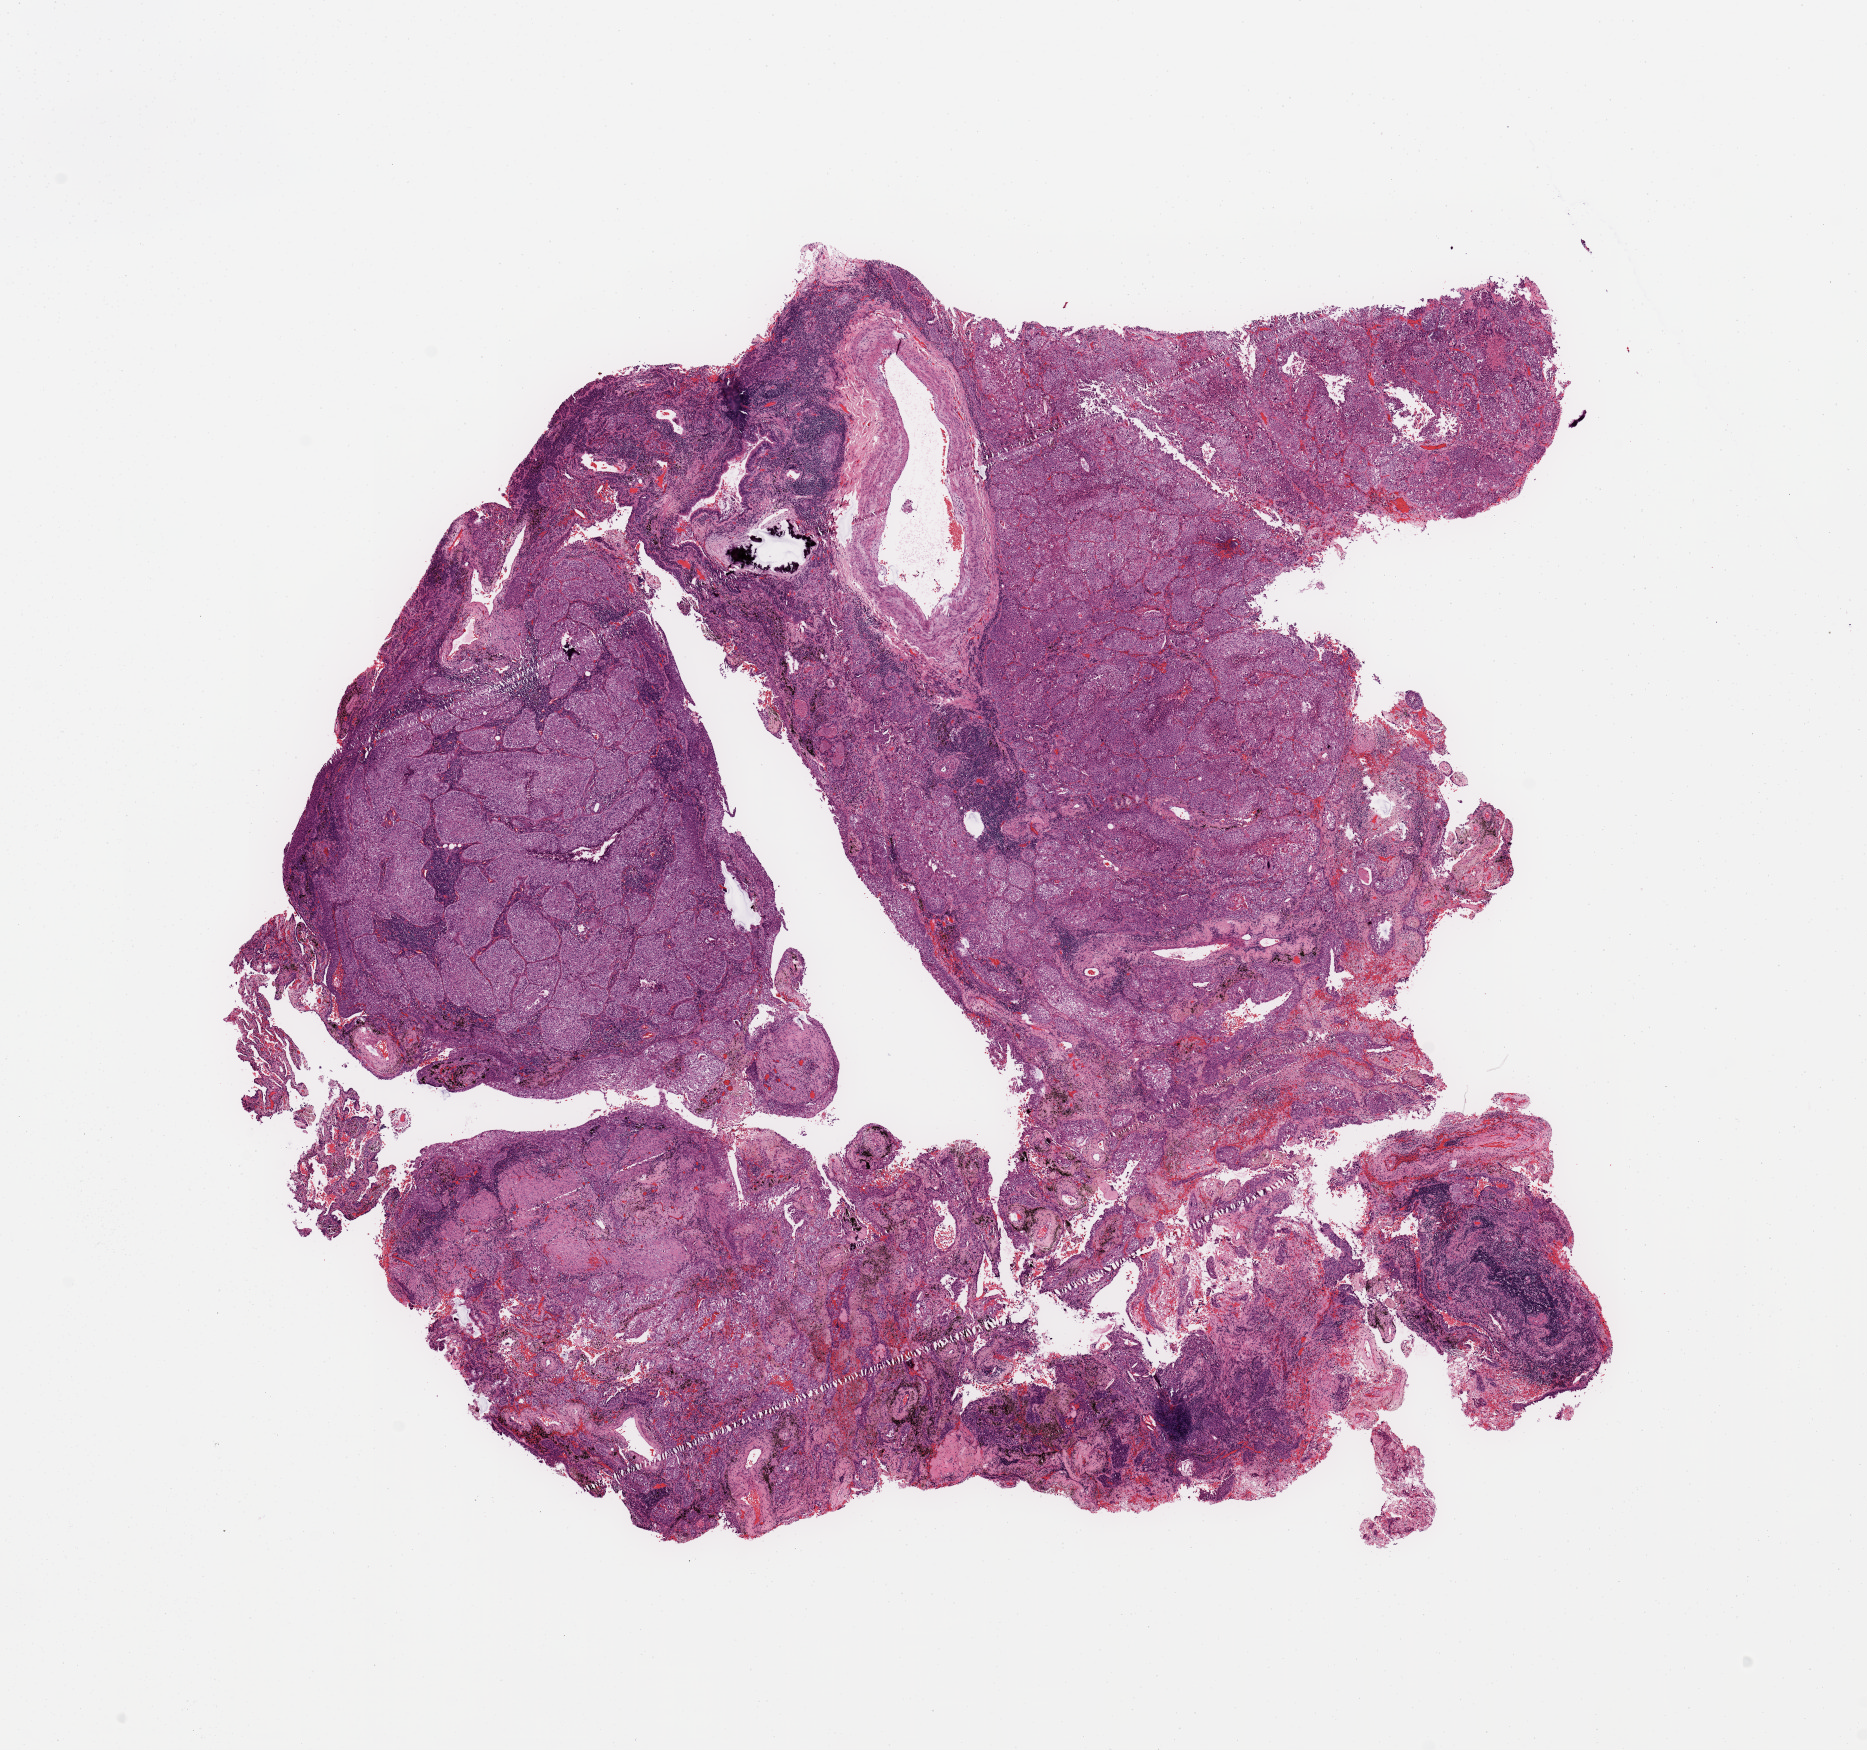
H&E whole-slide image — a low-resolution overview of the entire scanned area, about 14.8 x 13.8 mm (acquisition: 20x scan). Lung, tumour tissue. Patient: male, age 71 years. Histologic grade: G3 (poorly differentiated).
• diagnosis: Squamous cell carcinoma, NOS
• AJCC pathologic stage: IIB
• primary tumour site (as recorded): right lower lobe